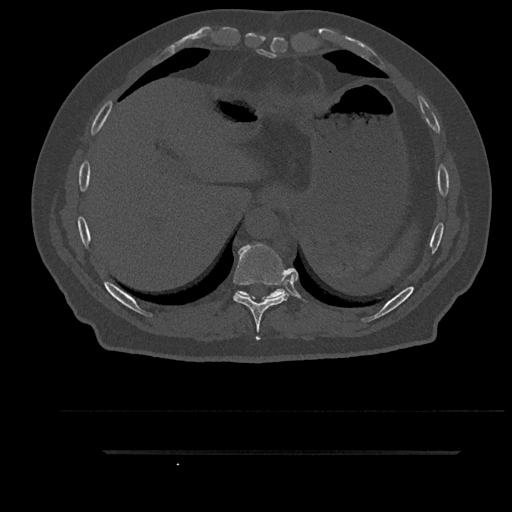
CT including the spine, one axial slice. Slice 409 of 797 in the series (ordered by position). Reconstruction kernel Br40s/3. 120 kVp. Bone window (W 1800 / L 400 HU). 0.5 mm slice thickness. 512 × 512 image matrix, field of view 432 × 432 mm. Male patient, age 63 years. Case-level facts recorded for this patient, not image findings: primary cancer: renal; vertebrae with lytic lesions (as recorded): T8.
Outlined on this slice (semi-automatically segmented with operator editing):
- T10 vertebra: bounding box [x1, y1, x2, y2] px = [236, 288, 286, 299]
- T9 vertebra: [233, 244, 290, 340]